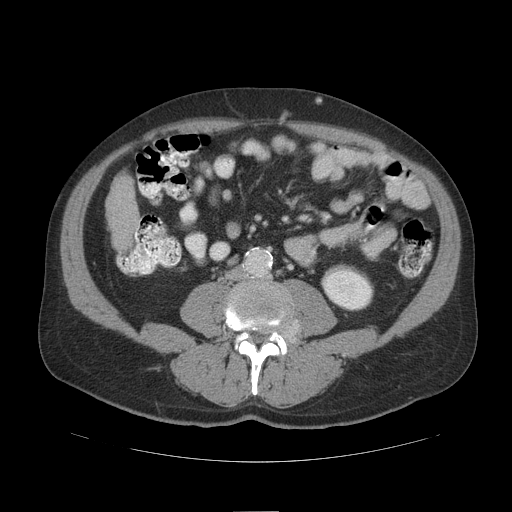
Contrast-enhanced abdominal CT (liver protocol), one axial slice. Position 23 of 109 along the scan axis. Reconstruction kernel STANDARD. Soft-tissue window (W 400 / L 40 HU). 2.5 mm slice thickness. 512 × 512 image matrix, field of view 420 × 420 mm. Case-level facts recorded for this patient, not image findings: diagnosis: hepatocellular carcinoma (patient treated with transarterial chemoembolisation; whether this scan precedes or follows treatment is not stated here); TNM stage (as recorded): Stage-IIIB; Child-Pugh class: A.
Structures marked on this image (semi-automatic segmentation, software-assisted and operator-edited):
- liver parenchyma outside the tumour (the mass and vessels are separate outlines, so this box may not span the whole liver): bounding box [x1, y1, x2, y2] px = [106, 174, 140, 250]